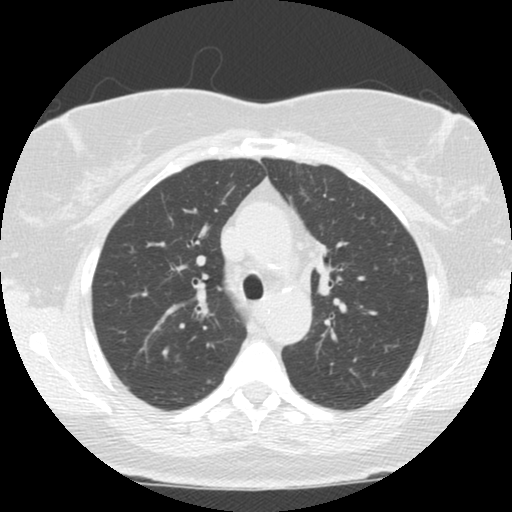
Low-dose screening chest CT, axial slice. Second screening round (one year after baseline). Lung window (W 1500 / L -600 HU). Standard (soft-tissue) reconstruction kernel (STANDARD). 120 kVp. Slice 42 of 120 in the series. Female, age 66 years at enrolment. Former smoker at enrolment.
Expert reader's lesion annotation, bounding box [x1, y1, x2, y2] px = [295, 234, 343, 292]. The exam's reader record, not a measurement of the box and not confirmed to be the same lesion: non-calcified nodule or mass ≥4 mm, left upper lobe, 12 × 9 mm, smooth margins, soft tissue attenuation, pre-existing on the prior screen: no. Official screen result: positive, other.